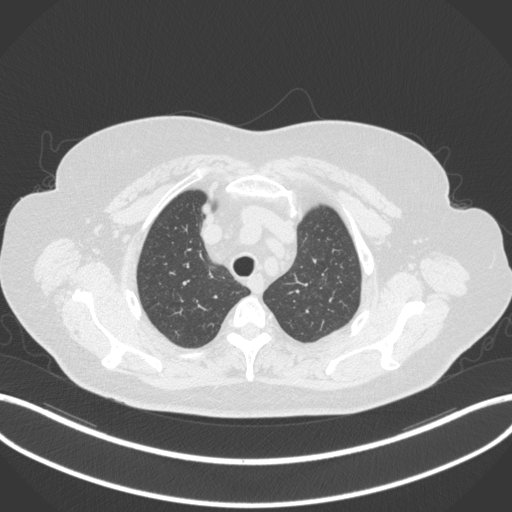
Chest CT, one axial slice. Slice 278 of 310 in the series (ordered by position). Reconstruction kernel B31f. Lung window (W 1500 / L -600 HU). 1 mm slice thickness. 512 × 512 image matrix, field of view 400 × 400 mm. Female patient, age 70 years. From the clinical record (not read from this slice): clinical TNM (as recorded): T1c N0 M0.
Structures marked on this image (bounding box drawn by a radiologist):
- lung tumour (recorded histology: adenocarcinoma): bounding box (x1, y1, x2, y2) in pixels: (317, 263, 332, 286)